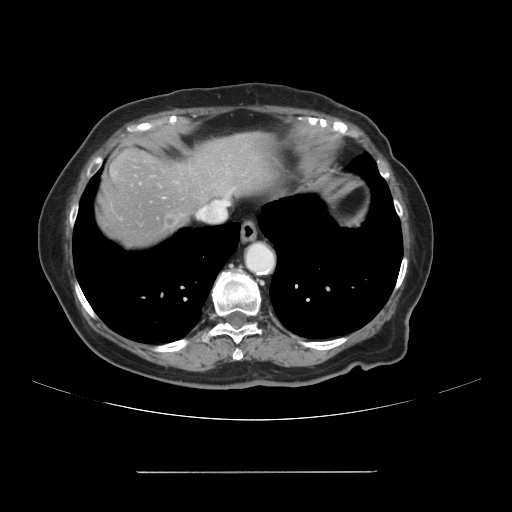
Contrast-enhanced abdominal CT, one axial slice; slice 98 of 111 in the series (ordered by position); intravenous contrast given; soft-tissue window (W 400 / L 40 HU); 512 × 512 image matrix, field of view 400 × 400 mm. Female patient, age 74 years. From the clinical record (not read from this slice): diagnosis: colorectal cancer liver metastases, imaged before liver resection.
Annotated regions visible in this slice (outlined manually by an expert reader):
- hepatic veins: bounding box [x1, y1, x2, y2] px = [216, 203, 224, 206]
- liver: [96, 134, 276, 253]
- planned liver remnant (the part of the liver to remain after resection): [194, 134, 275, 200]
- liver metastasis: [165, 214, 177, 226]